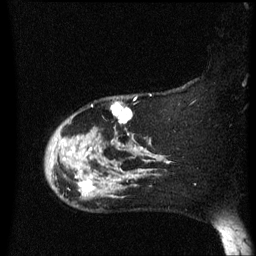
Breast MRI (dynamic contrast-enhanced), one sagittal slice. Slice 52 of 60 in the series (ordered by position). Dynamic contrast-enhanced series, image 2 of 3 at this slice position (ordered by acquisition). 1.5 T. TE 4.2 ms, TR 8.4 ms. 256 × 256 image matrix, field of view 200 × 200 mm. Female patient, age 47 years.
Structures marked on this image (semi-automatic segmentation, software-assisted and operator-edited):
- analysis volume of interest (the breast-tissue region the enhancement analysis was run in; not a lesion): bounding box [x1, y1, x2, y2] px = [46, 98, 149, 202]
- tumour enhancement mask (voxels above the 70 % enhancement threshold inside the analysis volume of interest): [68, 103, 143, 194]